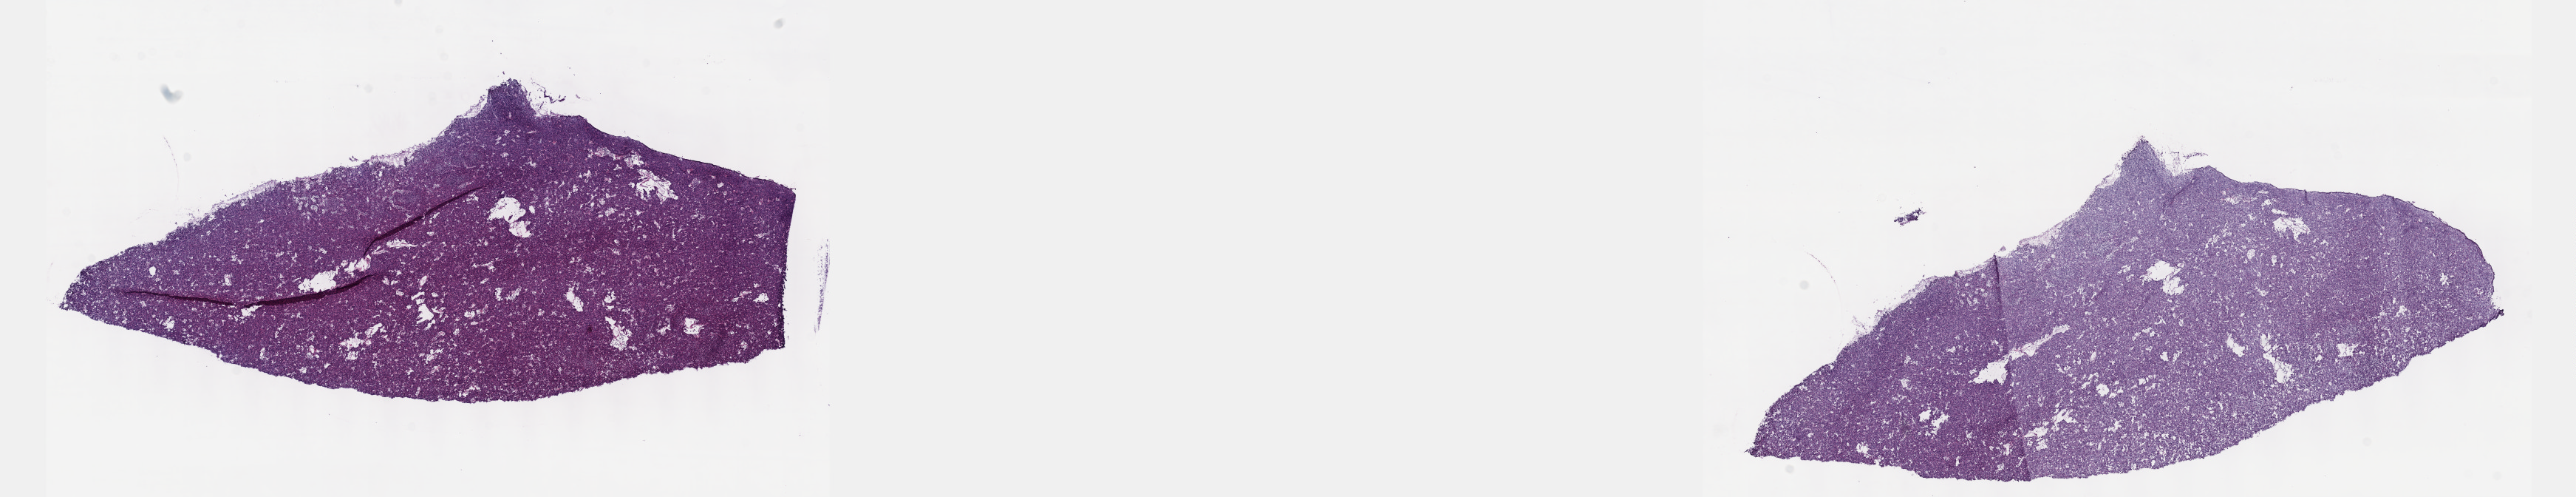
H&E-stained whole-slide image, low-resolution overview of the scanned area, about 28.2 x 5.4 mm (slide scanned at 40x). Frozen section from the top of the tissue portion. Sample: primary tumour, thymus. Patient: male, age at initial diagnosis 64 years. Slide review estimates, as recorded: tumour cells 95%, tumour nuclei 95%, normal cells 0%, stromal cells 5%, necrosis 0%. Inflammatory infiltration, as recorded: lymphocyte infiltration 0%, monocyte infiltration 0%, neutrophil infiltration 0%.
- pathologic diagnosis: Thymoma, type AB, malignant (anterior mediastinum)